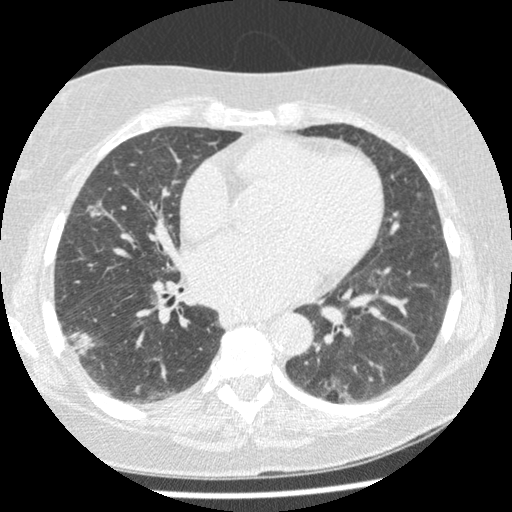
Low-dose screening chest CT, one axial slice. Slice 114 of 241 in the series (ordered by position). Reconstruction kernel STANDARD. 120 kVp. Lung window (W 1500 / L -600 HU). 1.25 mm slice thickness. 512 × 512 image matrix, field of view 305 × 305 mm.
Annotated regions visible in this slice (outlined manually by an expert reader):
- lesion 1 (tumor, lower lobe of right lung): box from (x=69, y=329) to (x=96, y=359) px